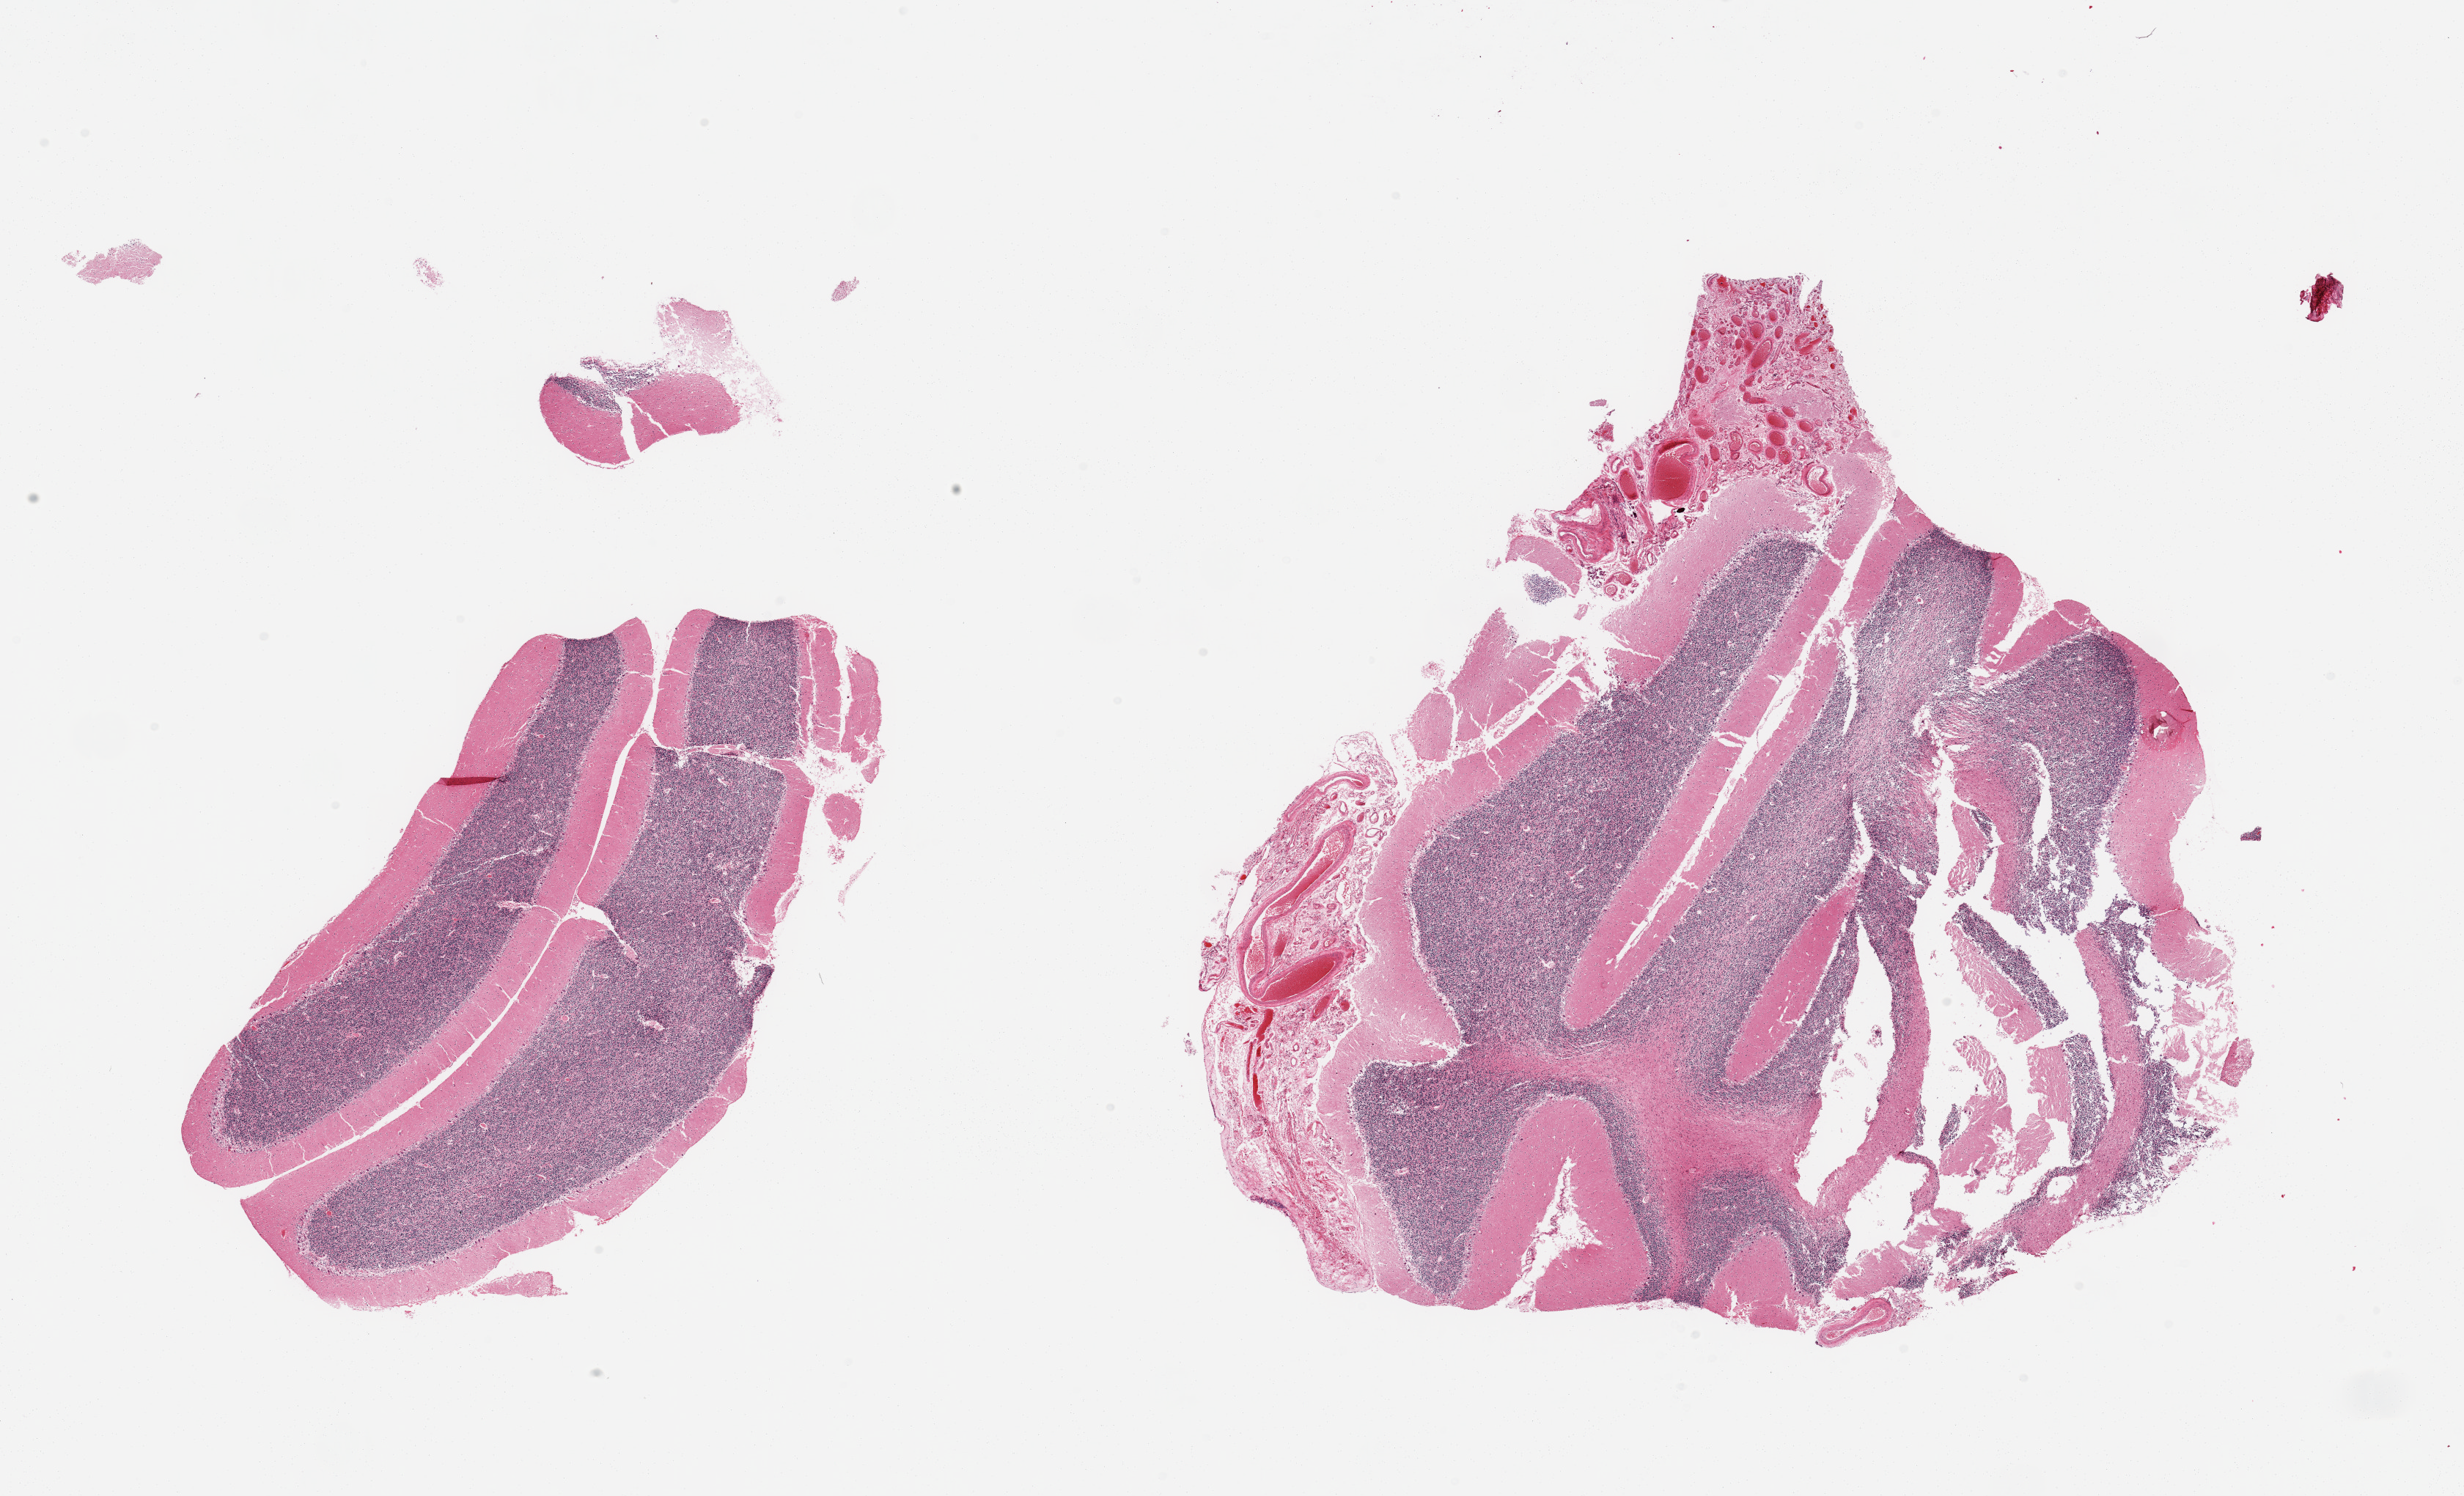
Haematoxylin and eosin whole-slide image, low-resolution overview of the scanned area, about 26.6 x 16.1 mm; PAXgene-fixed paraffin-embedded (PFPE) section; target tissue: cerebellum; donor tissue sample. Donor: male.
* pathologist's review note for this sample: 2 pieces (fragmented), mild to moderate autolysis, purkinje cells well visualized, significant attachment of meninges